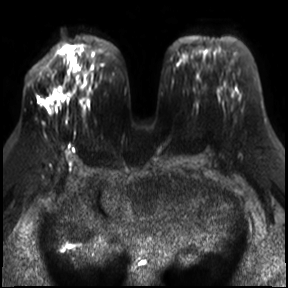
Breast MRI, one axial slice. Slice 15 of 30 in the series (ordered by position). Diffusion-weighted series; image 2 of 4 stored at this slice position (different b-values; order by instance number). 3 T. 4 mm slice thickness. 288 × 288 image matrix, field of view 340 × 340 mm. Female patient.
Annotated regions visible in this slice (outlined manually by an expert reader):
- tumour on diffusion-weighted imaging: bounding box <48,95,61,100> (left, top, right, bottom; pixels)